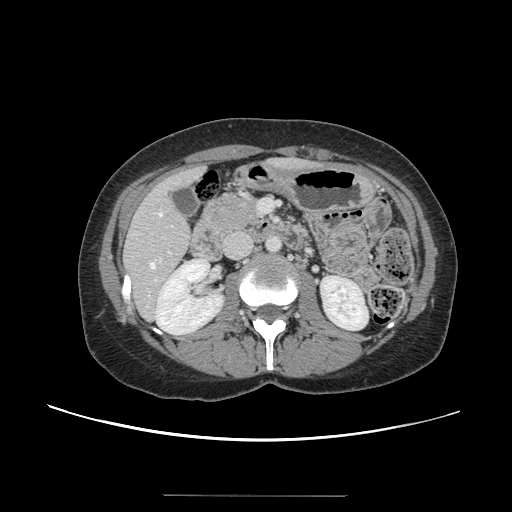
Contrast-enhanced abdominal CT, one axial slice; position 55 of 144 along the scan axis; 120 kVp; intravenous contrast given; soft-tissue window (W 400 / L 40 HU); 512 × 512 image matrix, field of view 380 × 380 mm. Female patient, age 53 years. Case-level facts recorded for this patient, not image findings: diagnosis: colorectal cancer liver metastases, imaged before liver resection; multiple liver metastases: yes; largest metastasis: 1.1 cm; chemotherapy before resection: no.
Outlined on this slice (expert manual segmentation):
- hepatic veins: bounding box (x1, y1, x2, y2) in pixels: (150, 212, 162, 268)
- liver: (125, 159, 312, 318)
- planned liver remnant (the part of the liver to remain after resection): (125, 159, 310, 312)
- portal vein (with intrahepatic branches): (154, 251, 172, 282)